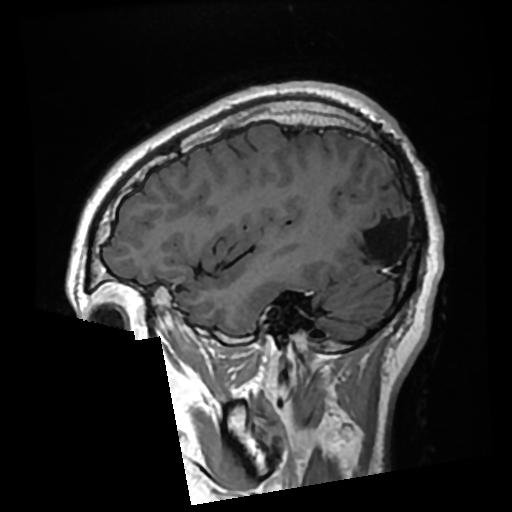
Brain MRI from a brain-tumour surgery series, one sagittal slice. Slice 81 of 276 in the series (ordered by position). T1-weighted post-contrast. 0.7 mm slice thickness. 512 × 512 image matrix, field of view 250 × 250 mm. Case-level facts recorded for this patient, not image findings: histopathology: Glioma with ependymal features; WHO grade: 2; tumour location: Left Parietal.
Structures marked on this image (expert manual segmentation):
- previous resection cavity: bounding box [x1, y1, x2, y2] px = [350, 216, 402, 263]